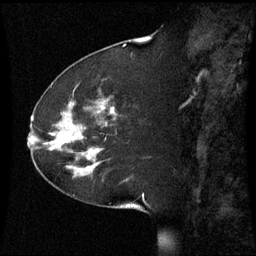
Breast MRI (dynamic contrast-enhanced), one sagittal slice. Dynamic contrast-enhanced series, image 2 of 3 at this slice position (ordered by acquisition). 1.5 T. TE 4.2 ms, TR 8.9 ms. 2.2 mm slice thickness. 256 × 256 image matrix, field of view 220 × 220 mm. Patient: female, 51 years. From the clinical record (not read from this slice): setting: breast cancer imaged before/during neoadjuvant chemotherapy; receptor status: HR-positive, HER2-negative.
Annotated regions visible in this slice (semi-automatic segmentation, software-assisted and operator-edited):
- analysis volume of interest (the breast-tissue region the enhancement analysis was run in; not a lesion): bounding box [x1, y1, x2, y2] px = [44, 102, 109, 169]
- tumour enhancement mask (voxels above the 70 % enhancement threshold inside the analysis volume of interest): [58, 108, 103, 169]